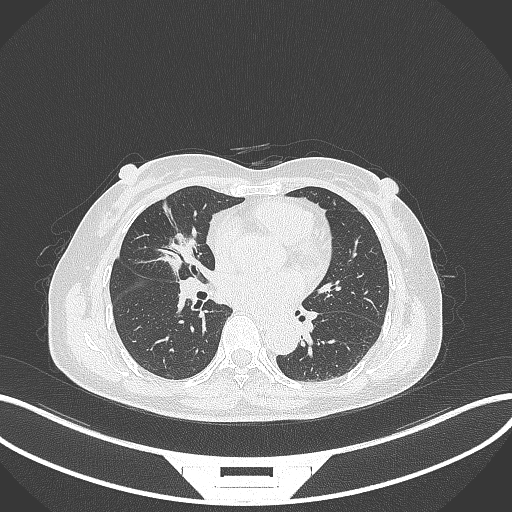
Chest CT, one axial slice. Position 144 of 284 along the scan axis. Lung window (W 1500 / L -600 HU). 1 mm slice thickness. 512 × 512 image matrix, field of view 400 × 400 mm. Patient: female, 51 years. Case-level facts recorded for this patient, not image findings: clinical TNM (as recorded): T1c N0 M0; histopathological grade: G2.
Outlined on this slice (rectangle marked by the reading radiologist):
- lung tumour (recorded histology: adenocarcinoma): bounding box <155,225,198,271> (left, top, right, bottom; pixels)